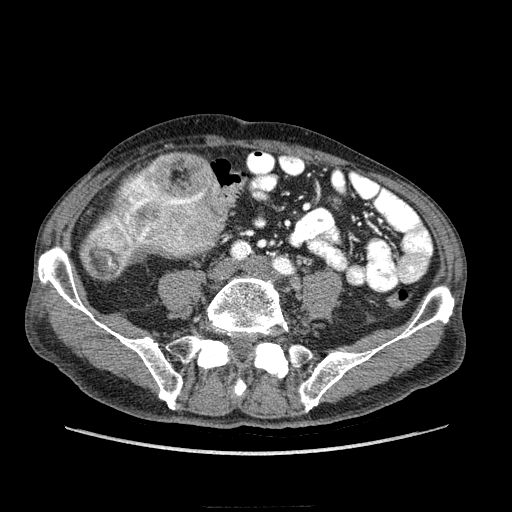
Contrast-enhanced abdominal CT (liver protocol), one axial slice; slice 27 of 218 in the series (ordered by position); reconstruction kernel STANDARD; 100 kVp; soft-tissue window (W 400 / L 40 HU); 2.5 mm slice thickness; 512 × 512 image matrix, field of view 380 × 380 mm. Case-level facts recorded for this patient, not image findings: diagnosis: hepatocellular carcinoma (patient treated with transarterial chemoembolisation; whether this scan precedes or follows treatment is not stated here); TNM stage (as recorded): Stage-IIIA; Child-Pugh class: A; tumour differentiation: well differentiated; tumour nodularity: multinodular.
Outlined on this slice (semi-automatically segmented with operator editing):
- mass: bounding box <79,152,236,281> (left, top, right, bottom; pixels)